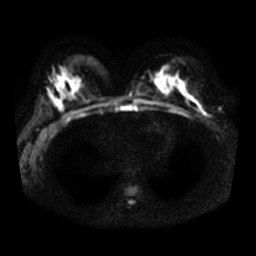
Breast MRI, one axial slice. Position 20 of 36 along the scan axis. Diffusion-weighted series; image 2 of 4 stored at this slice position (different b-values; order by instance number). 3 T. 256 × 256 image matrix, field of view 340 × 340 mm. Female patient.
Outlined on this slice (expert manual segmentation):
- tumour on diffusion-weighted imaging: bounding box <197,108,201,112> (left, top, right, bottom; pixels)